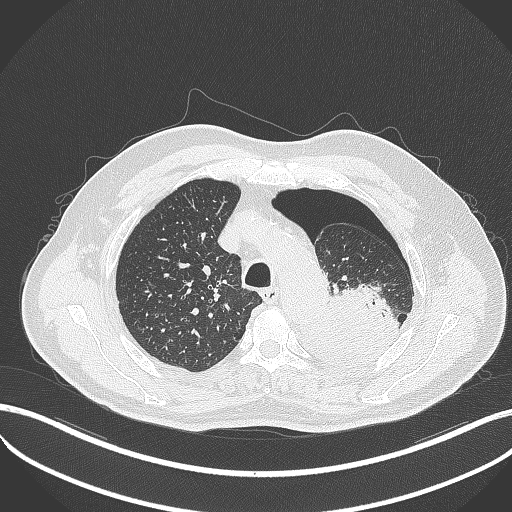
Chest CT, one axial slice; position 389 of 464 along the scan axis; lung window (W 1500 / L -600 HU); 1 mm slice thickness; 512 × 512 image matrix, field of view 400 × 400 mm. Patient: male, 76 years. From the clinical record (not read from this slice): clinical TNM (as recorded): T3 N0 M1b.
Outlined on this slice (rectangle marked by the reading radiologist):
- lung tumour (recorded histology: adenocarcinoma): bounding box <301,283,401,365> (left, top, right, bottom; pixels)